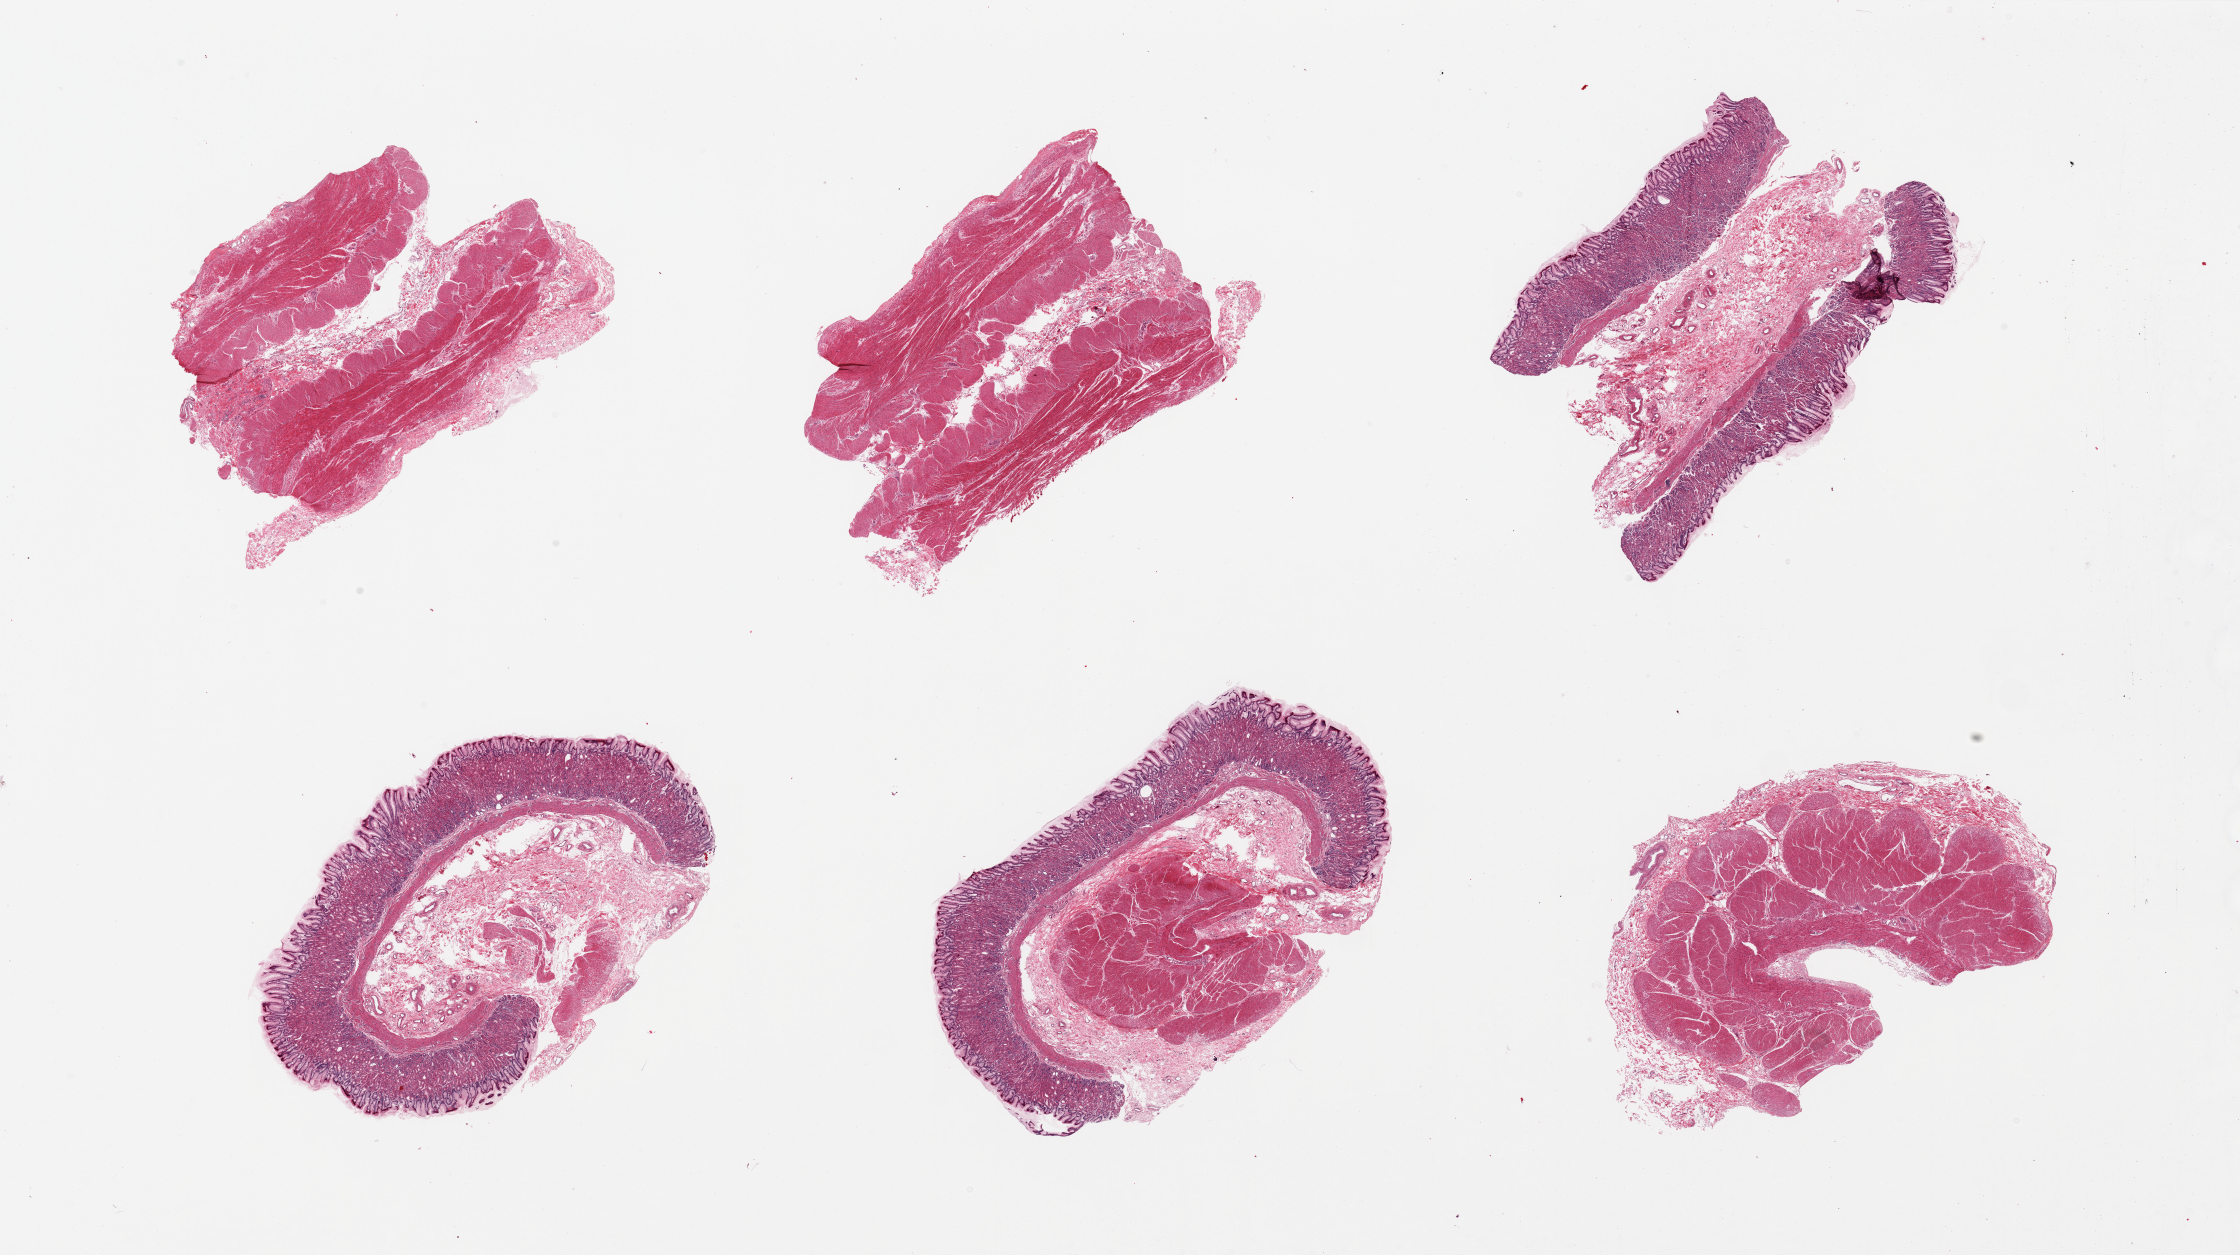
Haematoxylin and eosin whole-slide image — a low-resolution overview of the entire scanned area, about 35.4 x 19.9 mm. PAXgene-fixed paraffin-embedded (PFPE) section. Target tissue: stomach. Tissue donor sample. Donor sex: female.
- review note (as recorded): 6 pieces, 3 with mucosa, rest denuded (? sectioning/embedding artifact), mucosa up to 1mm thick, well- preserved